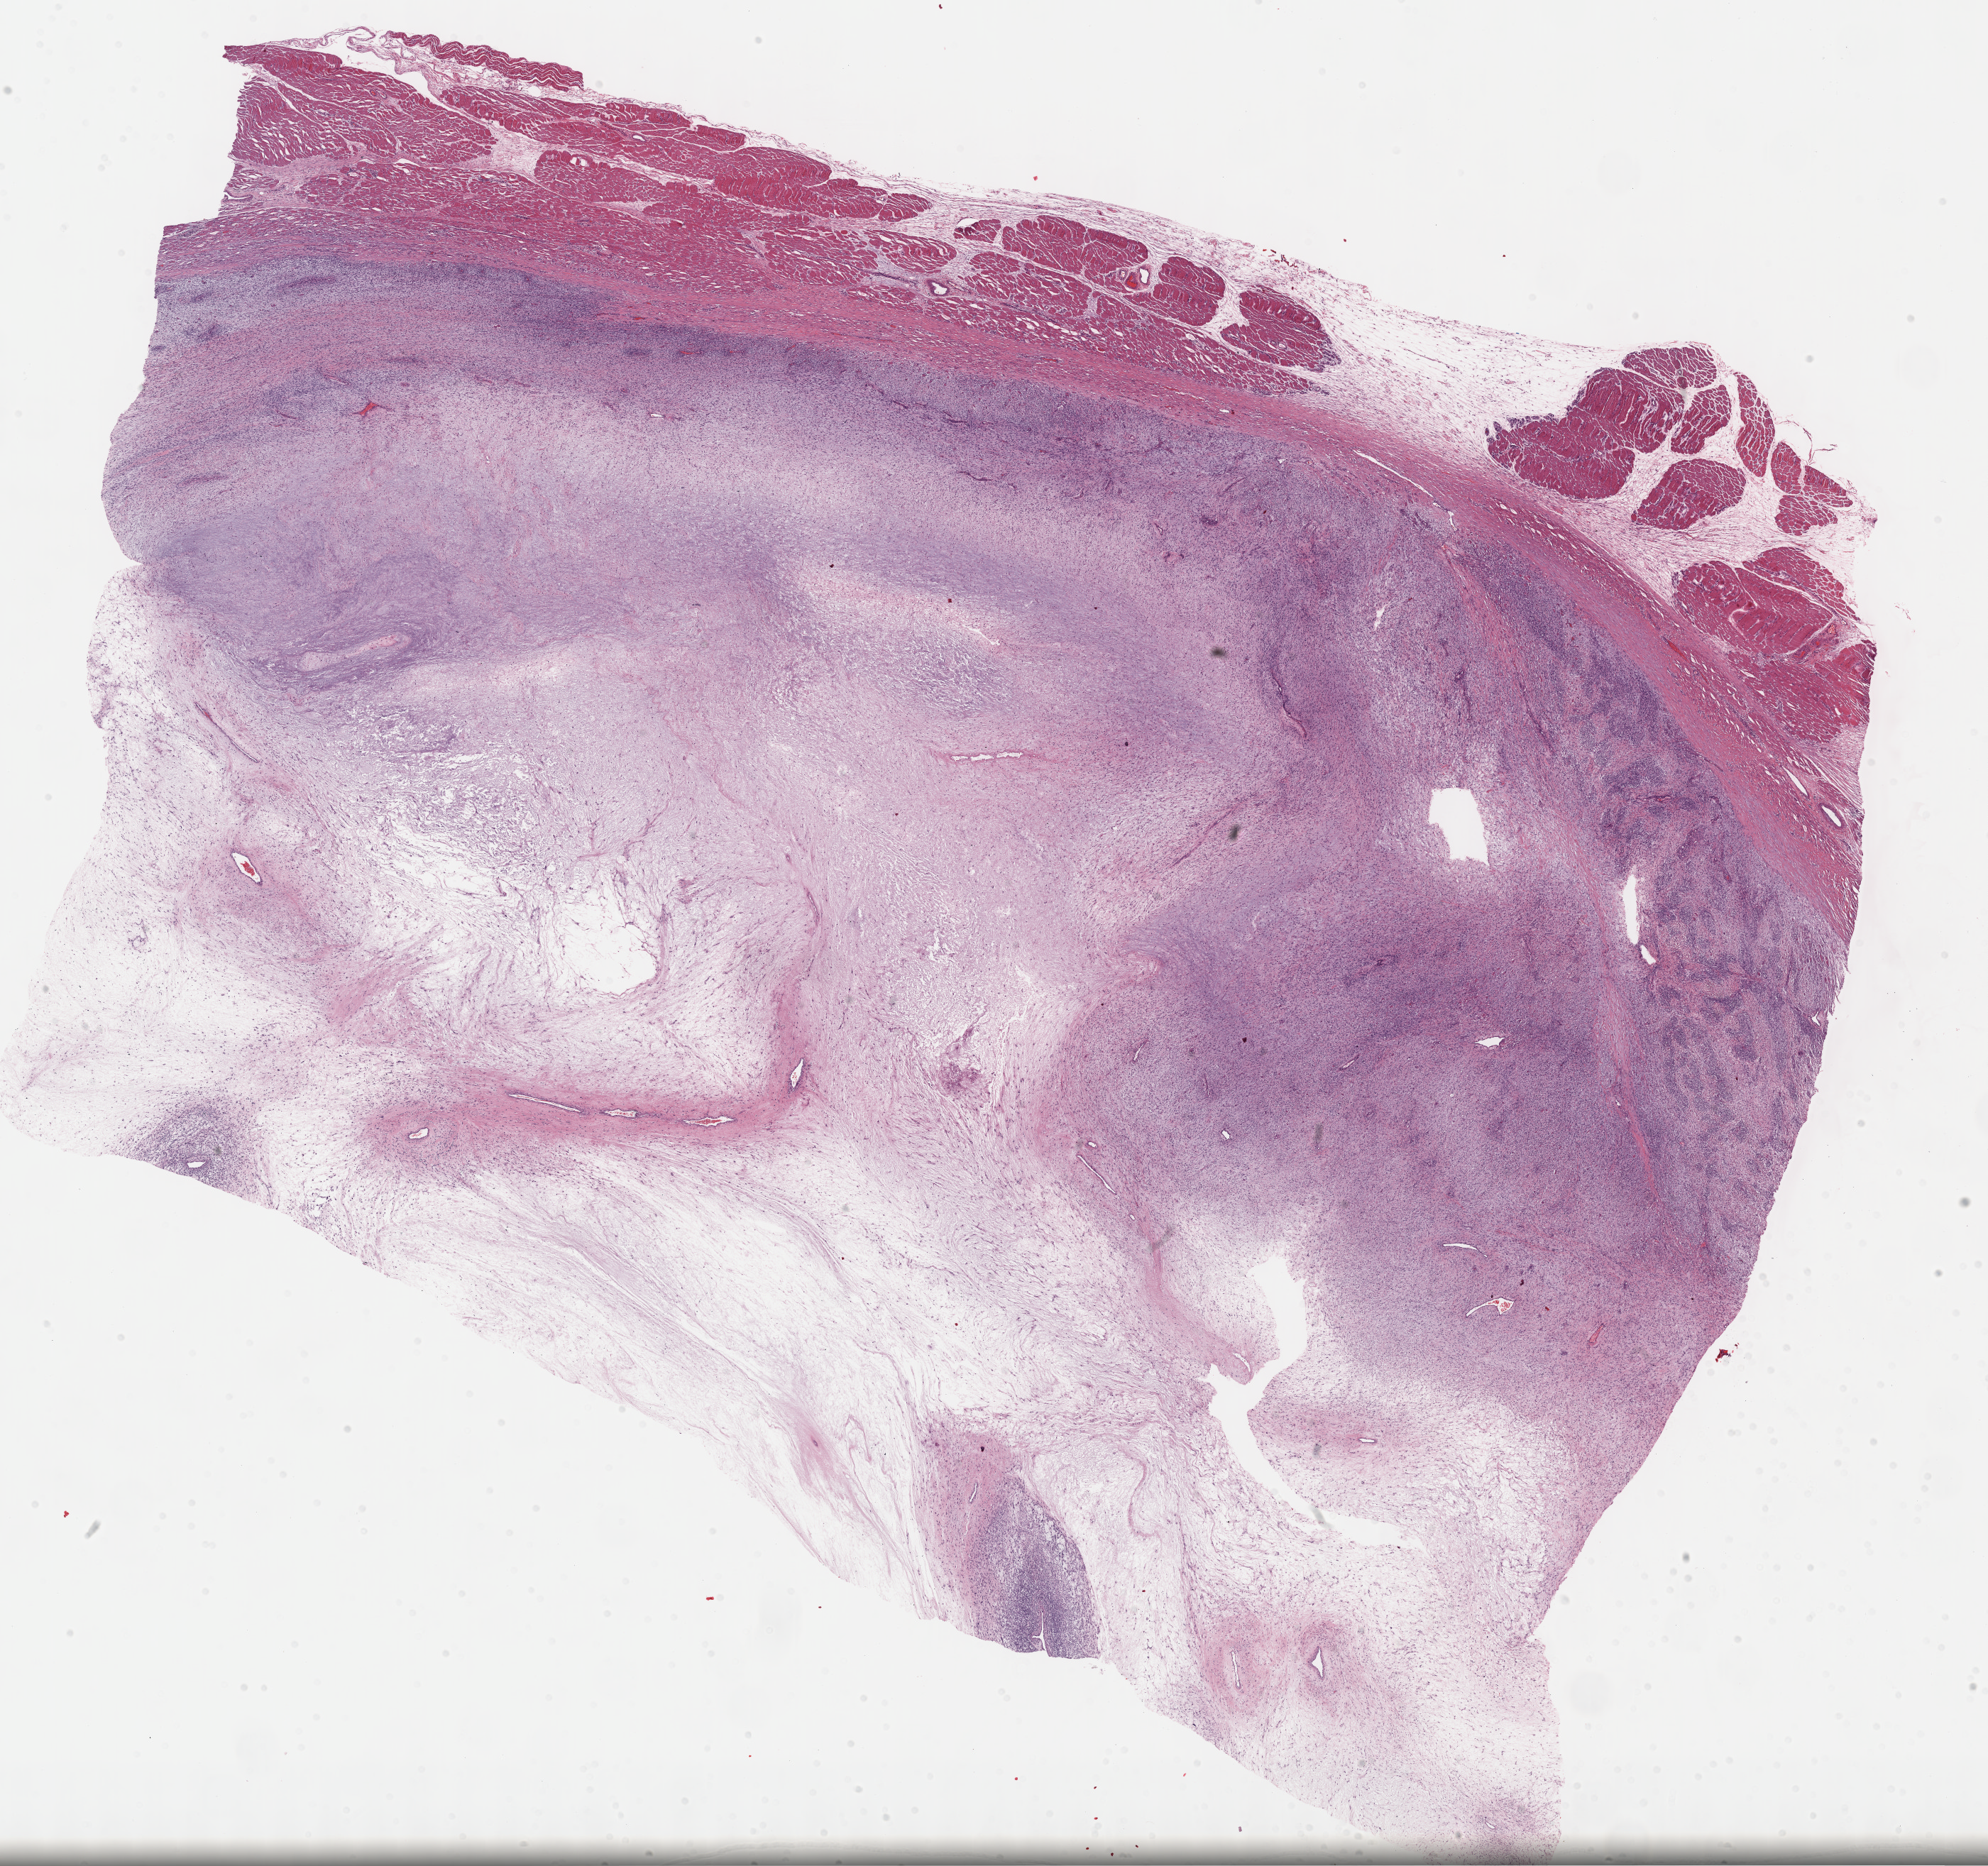
Whole-slide histology image, Hematoxylin and eosin (H&E) stained, shown as a low-resolution overview of the whole scanned area (about 22.7 x 21.3 mm). Formalin-fixed paraffin-embedded (FFPE) diagnostic section. Connective, subcutaneous and other soft tissues, primary tumour sample. Female patient; age at initial diagnosis 53 years.
* histologic diagnosis: Fibromyxosarcoma (connective, subcutaneous and other soft tissues of lower limb and hip)